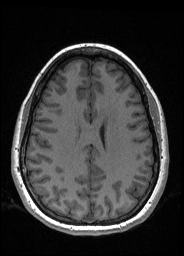
Pre-operative brain MRI before brain-tumour surgery, one axial slice. Position 71 of 176 along the scan axis. T1-weighted post-contrast. 1 mm slice thickness. 184 × 256 image matrix, field of view 180 × 250 mm. Case-level facts recorded for this patient, not image findings: histopathology: Oligodendroglioma; WHO grade: 2; IDH mutation: yes; tumour location: Left Frontal.
Outlined on this slice (expert manual segmentation):
- tumour: bounding box (x1, y1, x2, y2) in pixels: (100, 111, 106, 121)